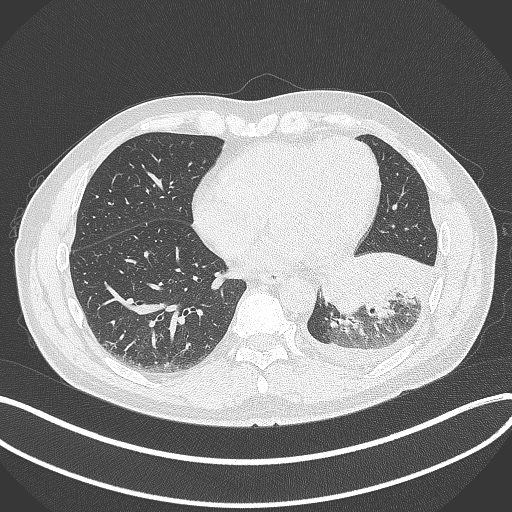
Chest CT, one axial slice. Slice 121 of 342 in the series (ordered by position). Reconstruction kernel B70f. 120 kVp. Lung window (W 1500 / L -600 HU). 1 mm slice thickness. 512 × 512 image matrix, field of view 400 × 400 mm. Male patient, age 58 years. Case-level facts recorded for this patient, not image findings: clinical TNM (as recorded): T3 N1 M1b; histopathological grade: G3.
Structures marked on this image (bounding box drawn by a radiologist):
- lung tumour (recorded histology: small cell carcinoma): box from (x=317, y=247) to (x=433, y=315) px